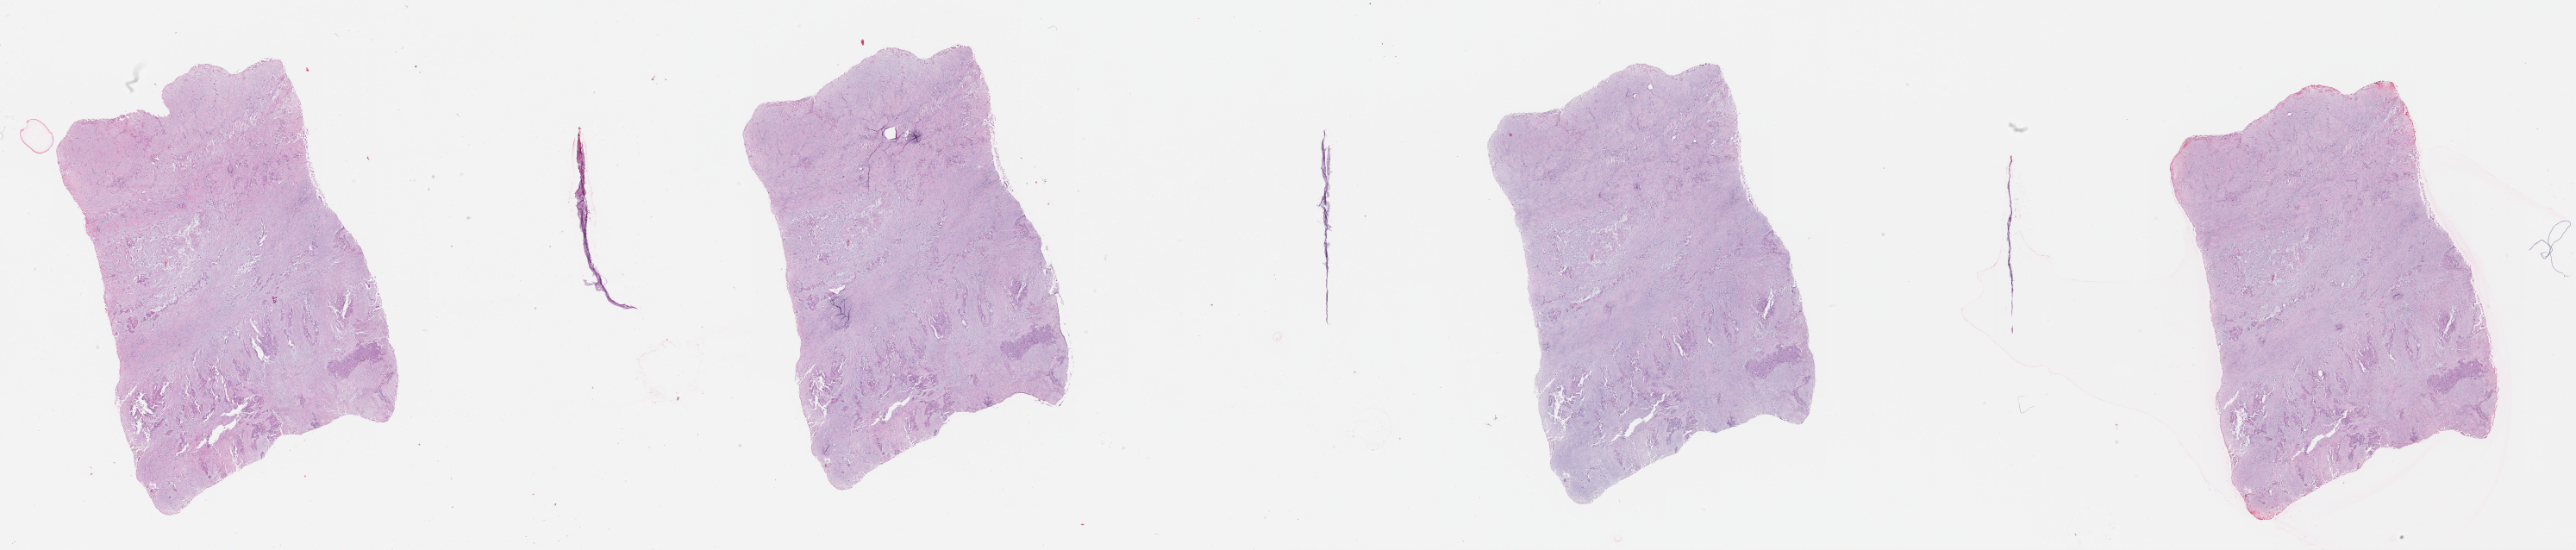
Whole-slide histology image, H&E-stained, shown as a low-resolution overview of the whole scanned area (about 48.1 x 10.3 mm); lung, tumour tissue. Patient: male, age 74 years.
* patient diagnosis (cohort enrolment): squamous cell carcinoma (lung)